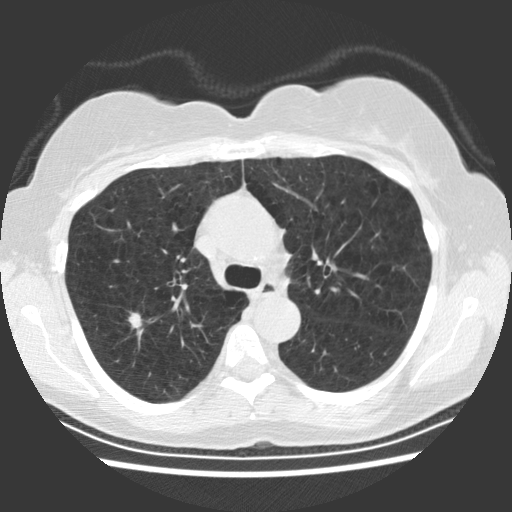
Axial slice from a low-dose chest CT screening exam; baseline annual screen; lung window (W 1500 / L -600 HU); standard (soft-tissue) reconstruction kernel (STANDARD); 120 kVp; slice 73 of 234 in the series; 512 × 512 image matrix. Female, age 66 years at enrolment.
Lesion marked by an expert reader, bounding box (x1, y1, x2, y2) in pixels: (111, 302, 153, 340). Screening reader's record for this exam (one nodule recorded; not confirmed to be the boxed lesion): non-calcified nodule or mass ≥4 mm, right upper lobe, 10 × 8 mm, smooth margins, soft tissue attenuation. Official screen result: positive, change unspecified: nodule(s) >= 4 mm or enlarging nodule(s), mass(es), or other non-specific abnormalities suspicious for lung cancer. Later outcome: lung cancer diagnosed 54 days after this screen — squamous cell carcinoma, keratinizing, NOS, right upper lobe, poorly differentiated (G3), stage IA (AJCC 6th edition), 11 mm at pathology.